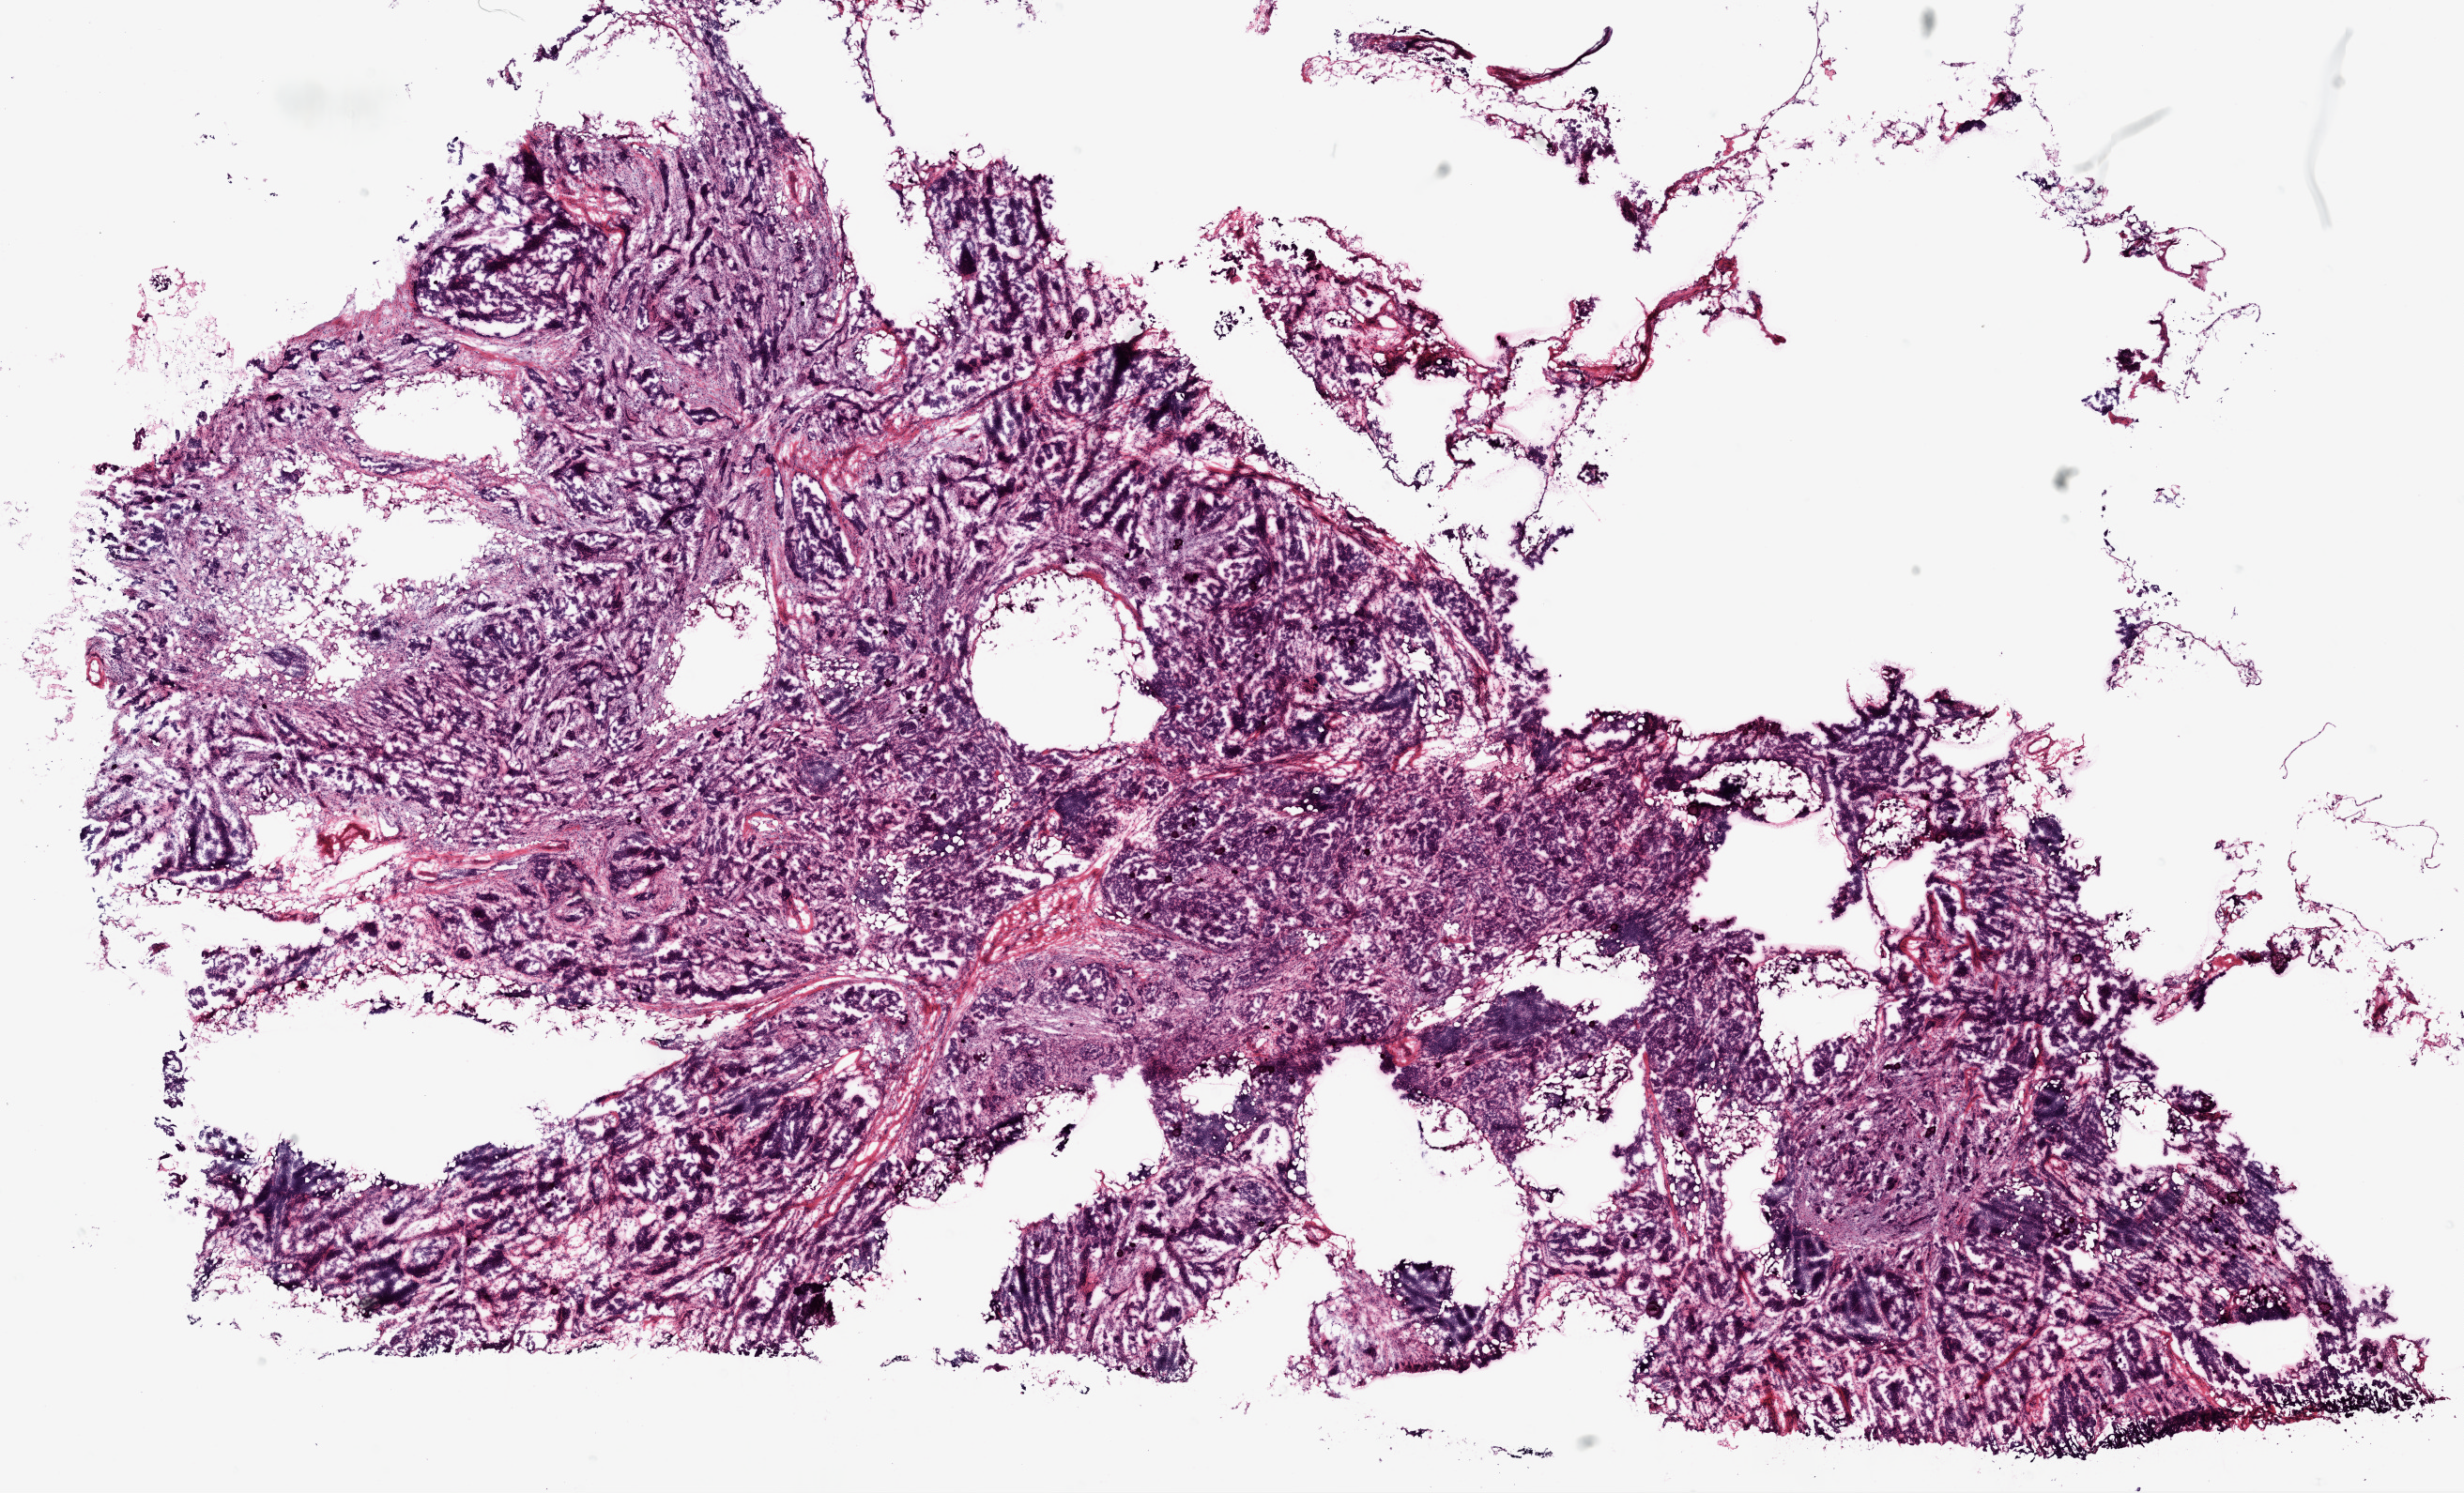
Digitized Hematoxylin and eosin (H&E) stained tissue section (whole slide) — low-resolution overview of the scanned area, about 21.1 x 12.8 mm (slide scanned at 20x). Frozen section from the top of the tissue portion. Sample: primary tumour, ovary. Patient: female, age at initial diagnosis 56 years. Histologic grade: G3 (poorly differentiated). Composition of this section per pathologist review: tumour cells 79%, tumour nuclei 80%, normal cells 0%, stromal cells 20%, necrosis 1%.
Pathologic diagnosis: Serous cystadenocarcinoma, NOS. FIGO stage: IIIC.